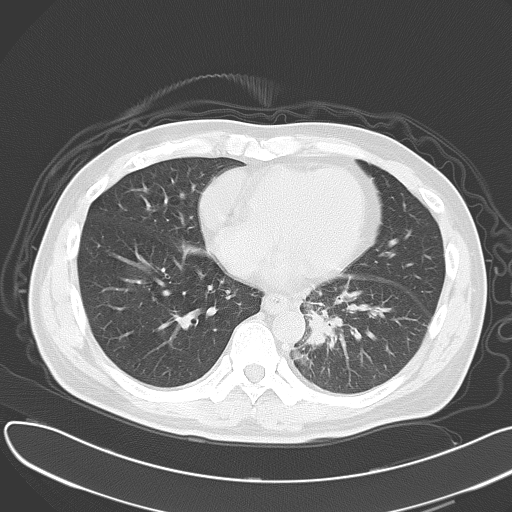
Chest CT, one axial slice. Position 19 of 55 along the scan axis. 120 kVp. Lung window (W 1500 / L -600 HU). 5 mm slice thickness. 512 × 512 image matrix. Male patient, age 55 years. Case-level facts recorded for this patient, not image findings: clinical TNM (as recorded): T2 N3 M0; histopathological grade: G3.
Outlined on this slice (bounding box drawn by a radiologist):
- lung tumour (recorded histology: small cell carcinoma): bounding box [x1, y1, x2, y2] px = [300, 306, 337, 361]